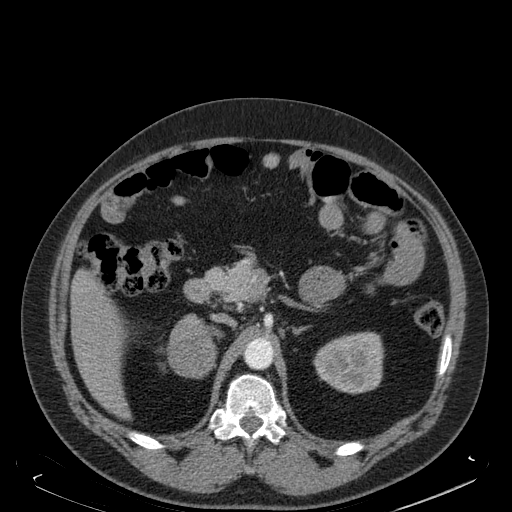
Contrast-enhanced abdominal CT, one axial slice; position 107 of 181 along the scan axis; soft-tissue window (W 400 / L 40 HU); 512 × 512 image matrix, field of view 405 × 405 mm. Male patient. From the clinical record (not read from this slice): diagnosis: adrenocortical carcinoma; tumour side: right adrenal; tumour size at pathology: 7.5 cm; Ki-67 index: 25 %; stage (as recorded): 4.
Annotated regions visible in this slice (semi-automatically segmented with operator editing):
- mass: box from (x=168, y=314) to (x=215, y=379) px